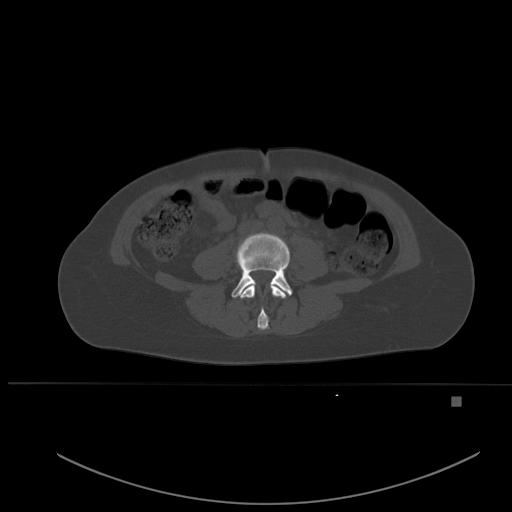
CT including the spine, one axial slice. Slice 180 of 651 in the series (ordered by position). Bone window (W 1800 / L 400 HU). 512 × 512 image matrix, field of view 443 × 443 mm. Female patient, age 49 years. Case-level facts recorded for this patient, not image findings: primary cancer: breast; vertebrae with lytic lesions (as recorded): L3, T12, L4.
Outlined on this slice (semi-automatic segmentation, software-assisted and operator-edited):
- L3 vertebra: bounding box [x1, y1, x2, y2] px = [240, 285, 286, 330]
- L4 vertebra: [231, 233, 293, 298]